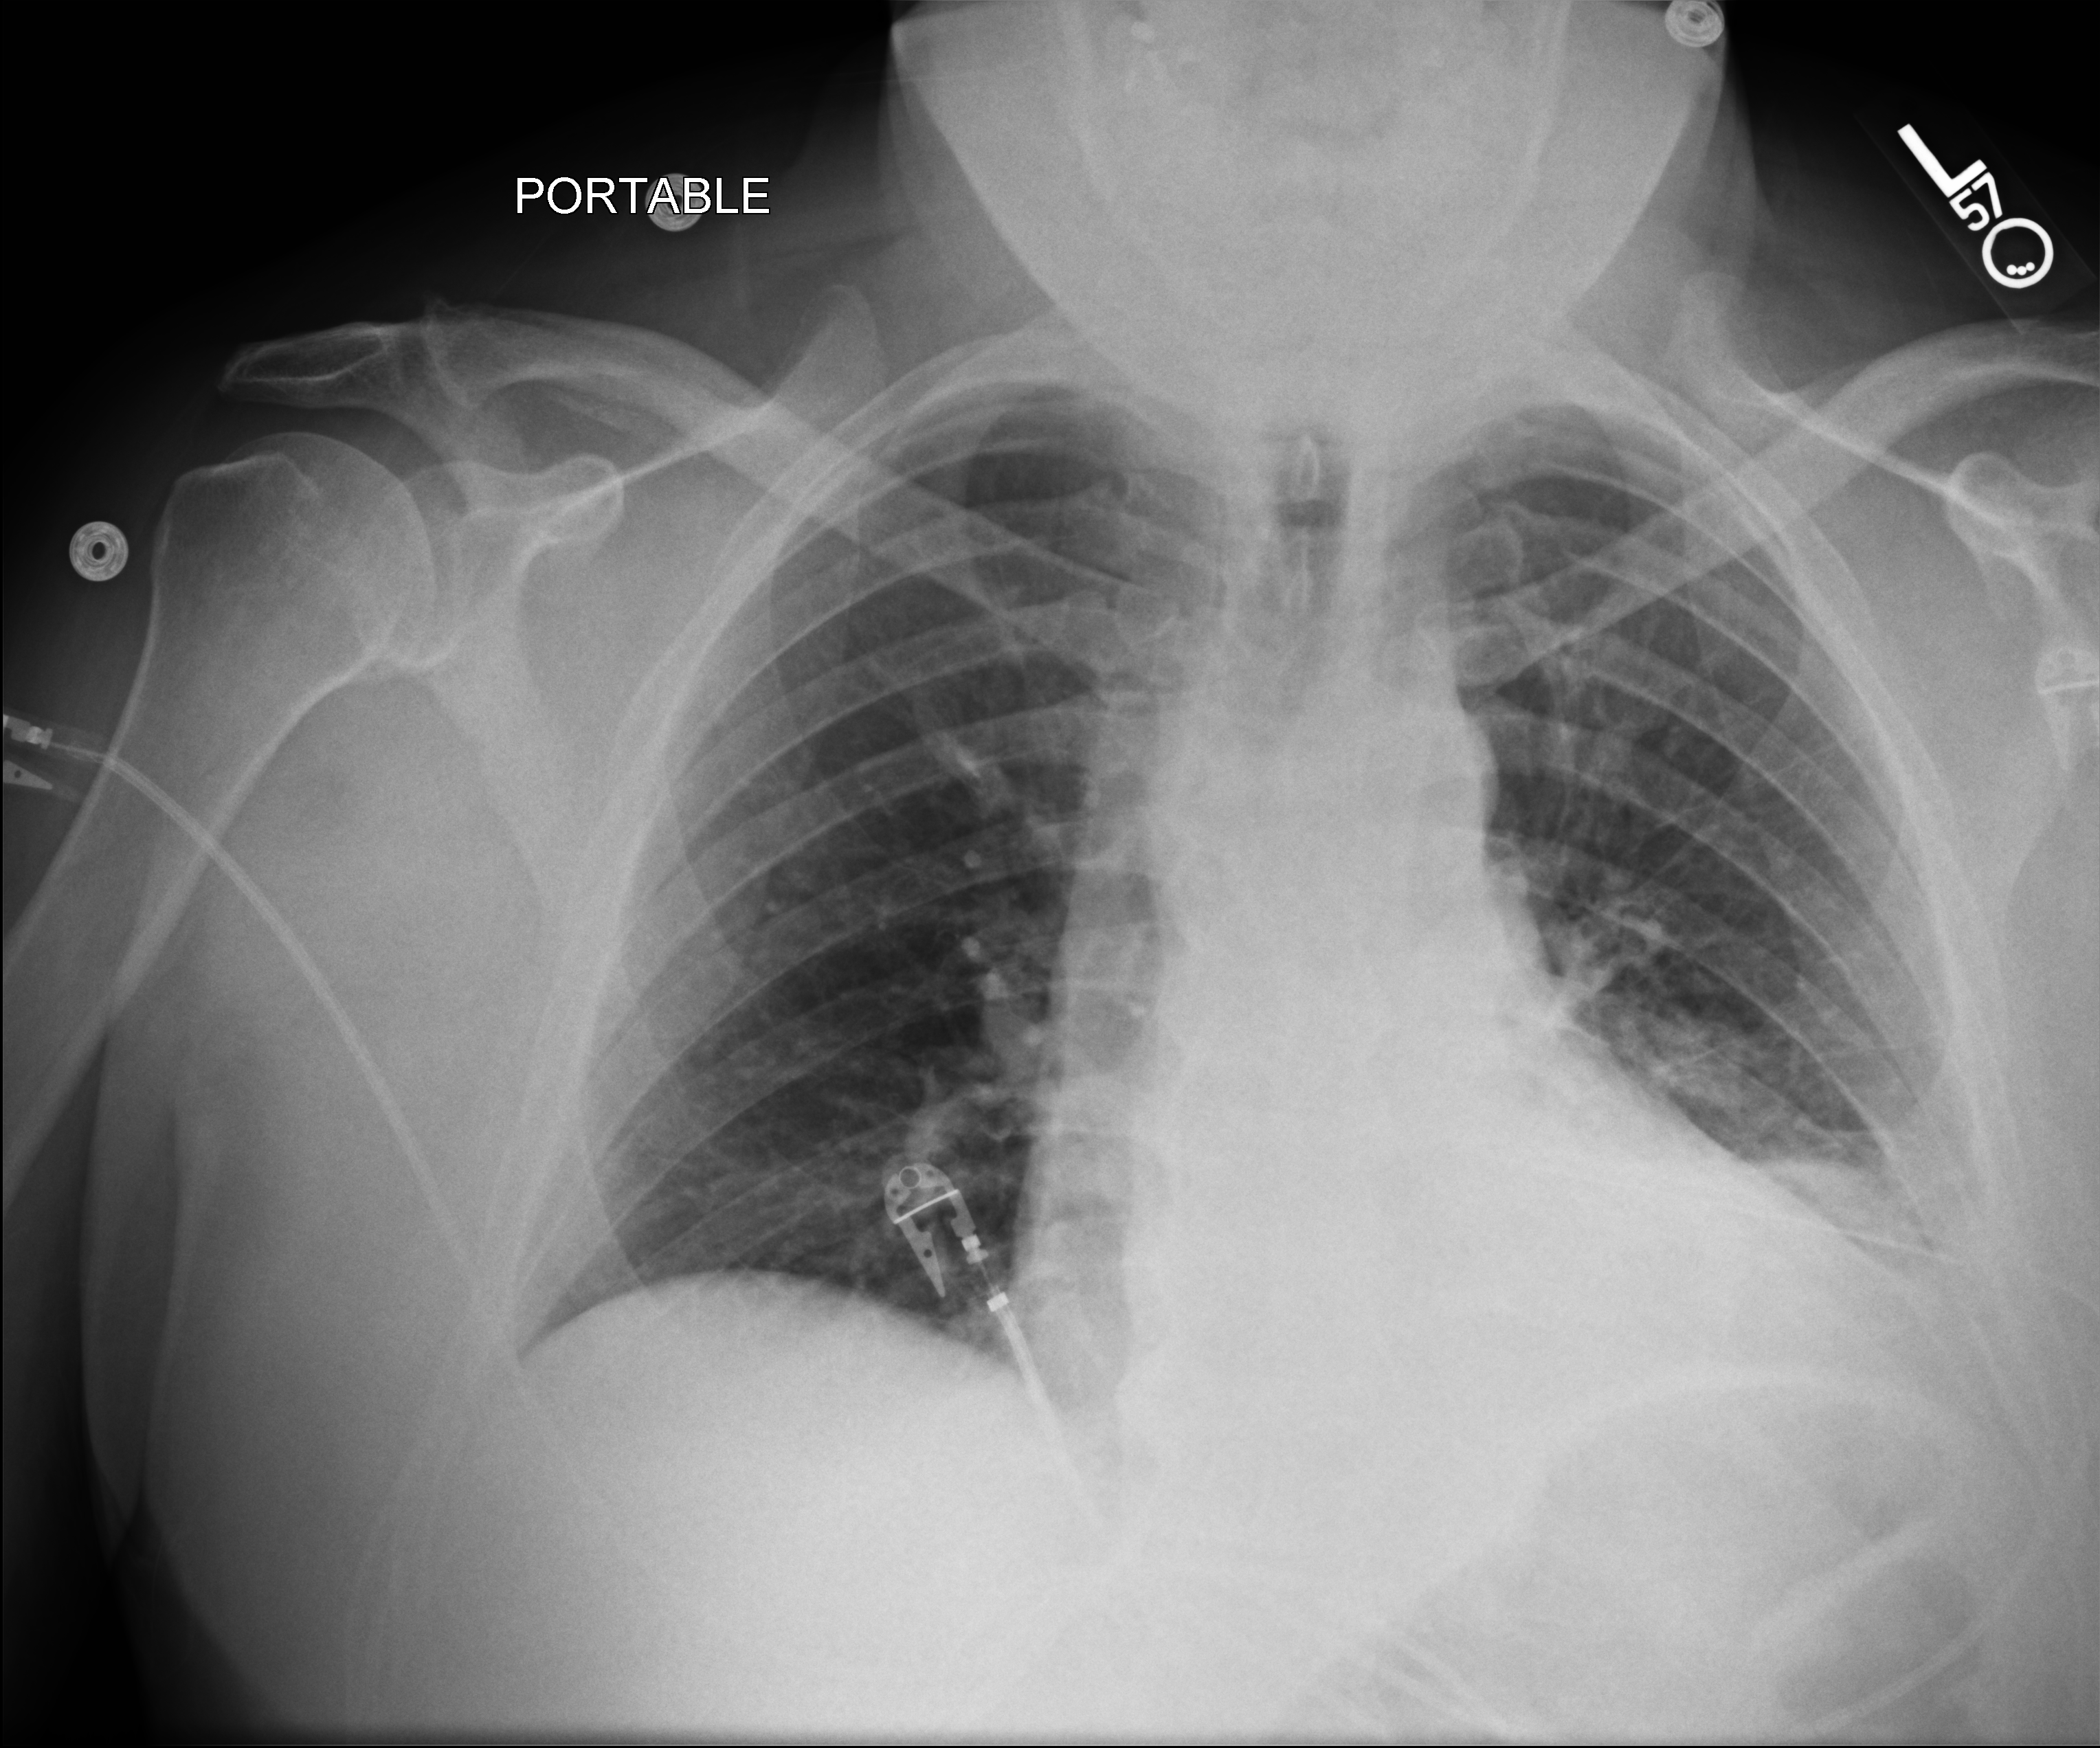
Bedside chest radiograph (computed radiography); anteroposterior (AP) projection. Patient hospitalised with COVID-19; male, aged 18–59 years.
From the hospital-stay record, not from the radiograph (when in the stay this image was taken is not recorded): mechanically ventilated during this hospital stay: no.